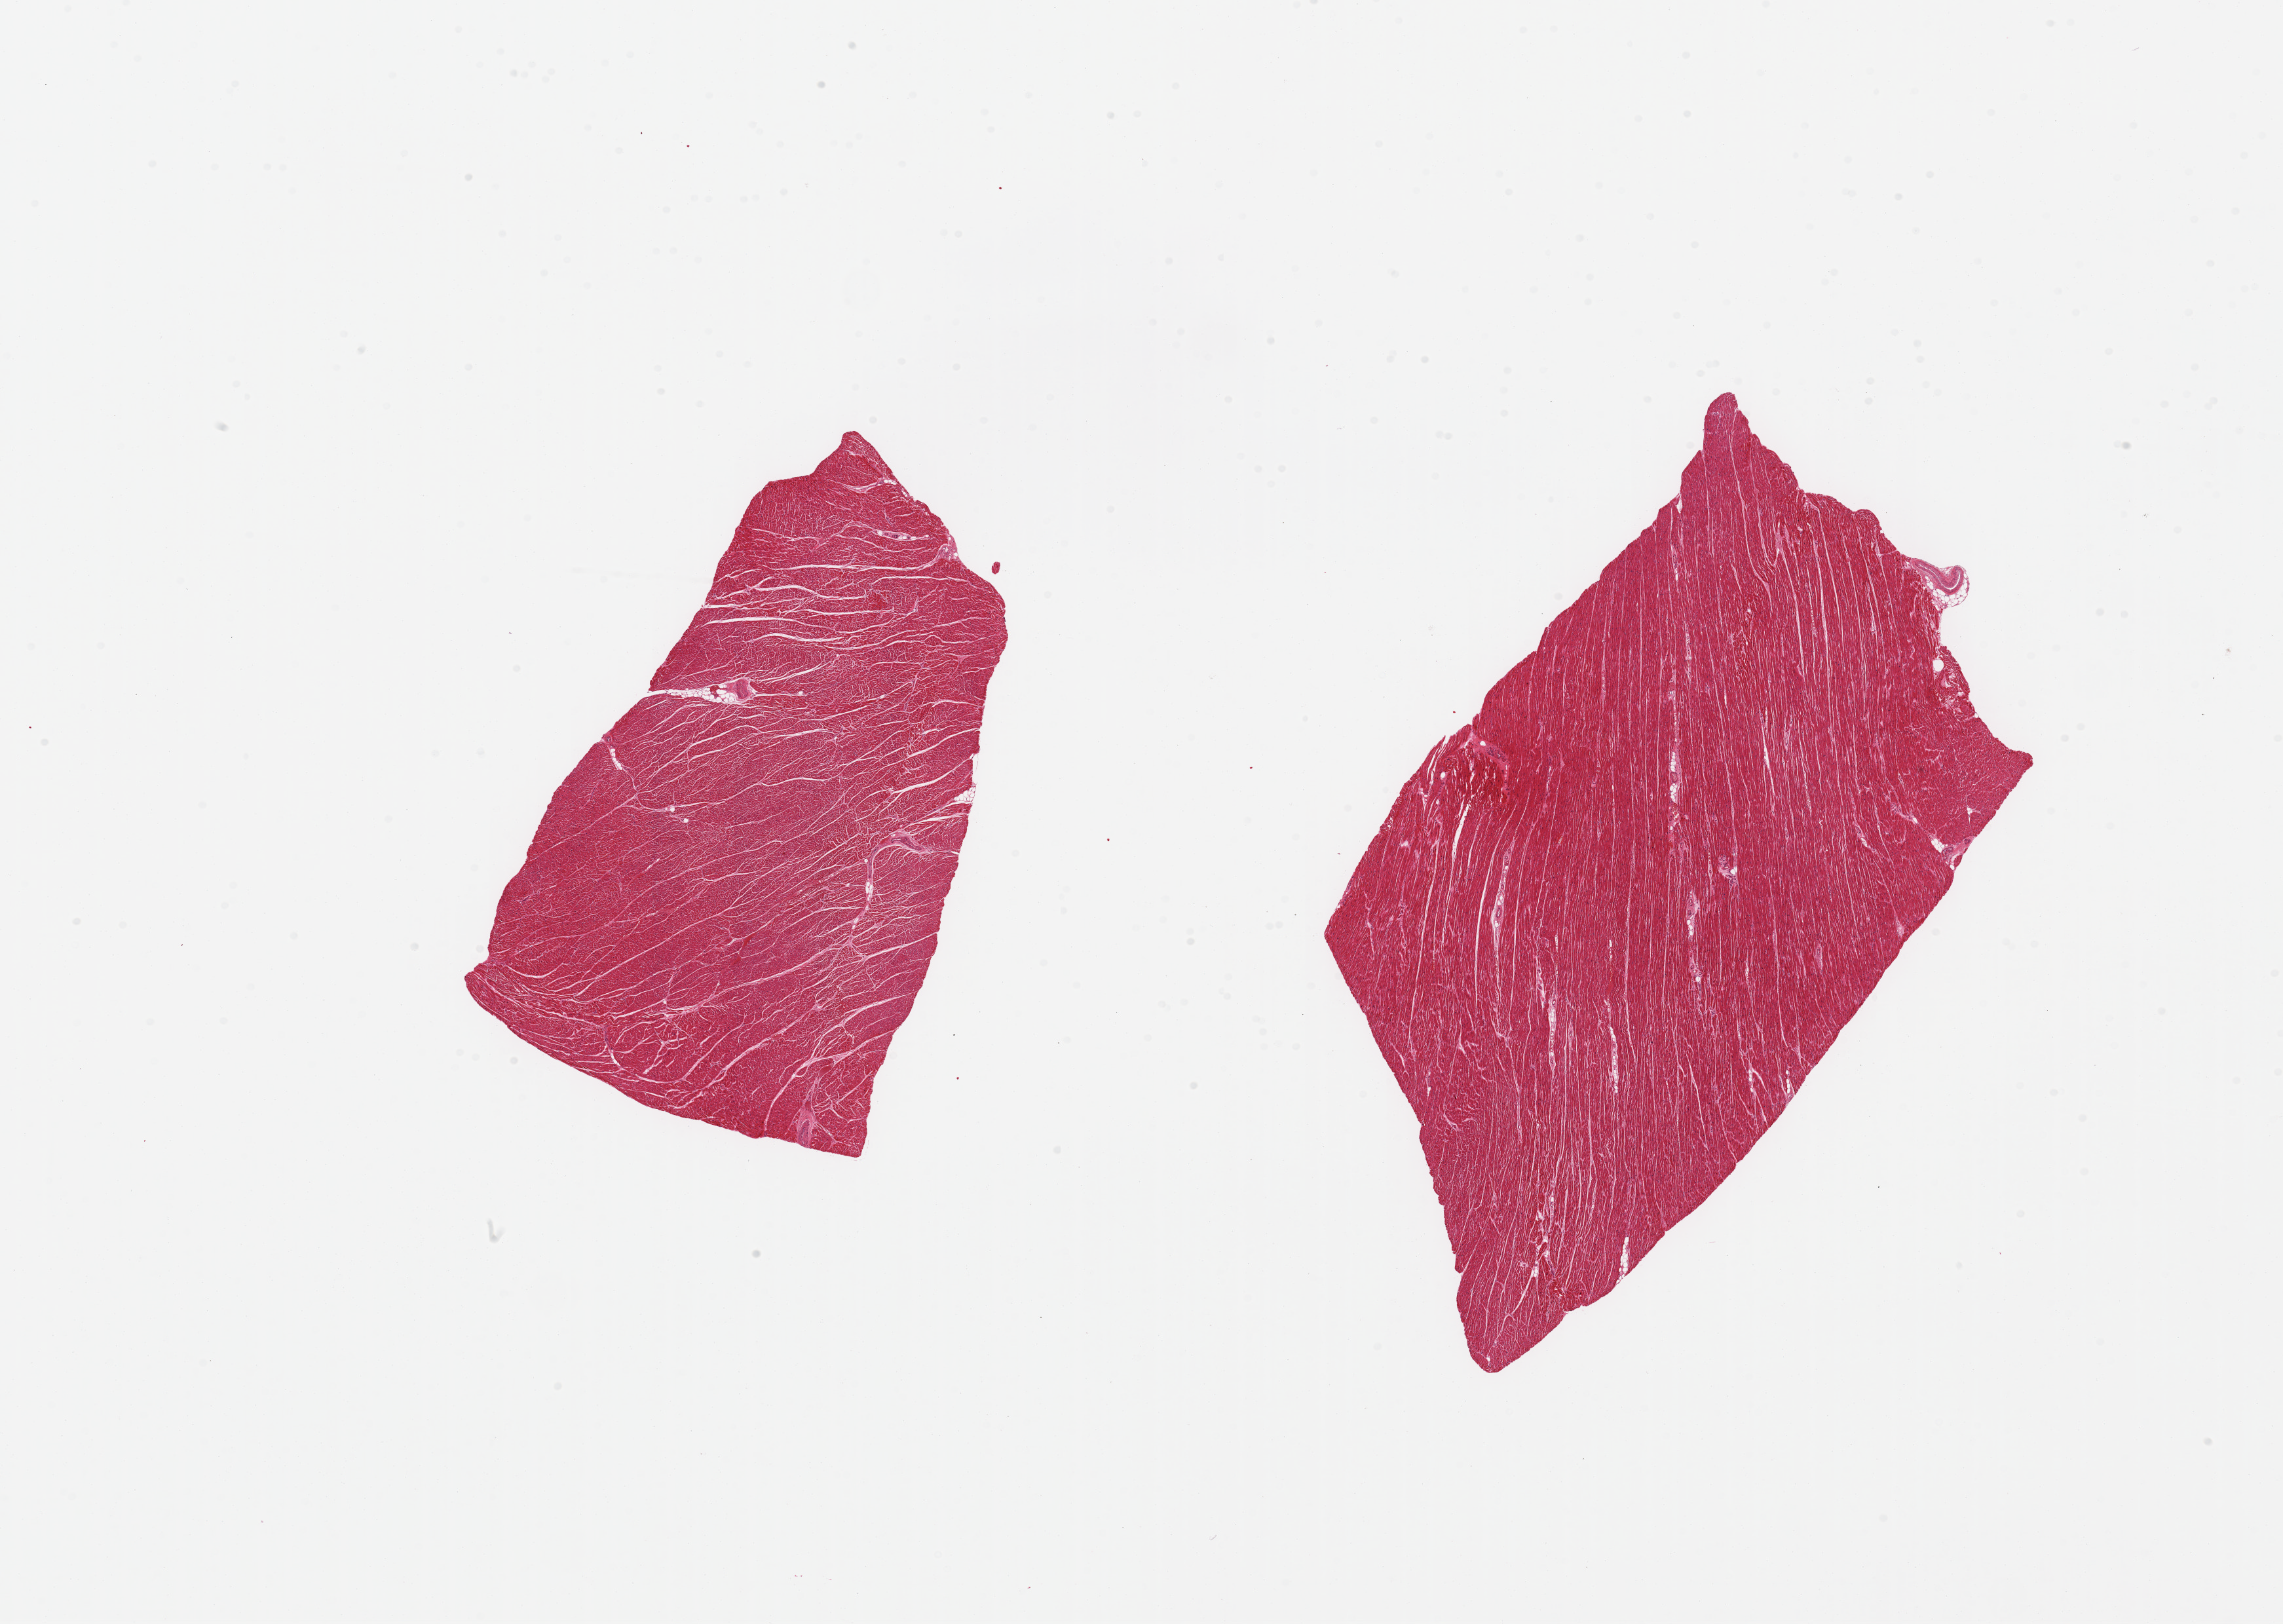
Digitized haematoxylin and eosin-stained section, whole scanned area (about 27.6 x 19.6 mm) shown as a low-resolution overview, PAXgene-fixed paraffin-embedded (PFPE) section, target tissue: heart, tissue donor sample.
Reviewer comment on this tissue sample: 2 pieces.